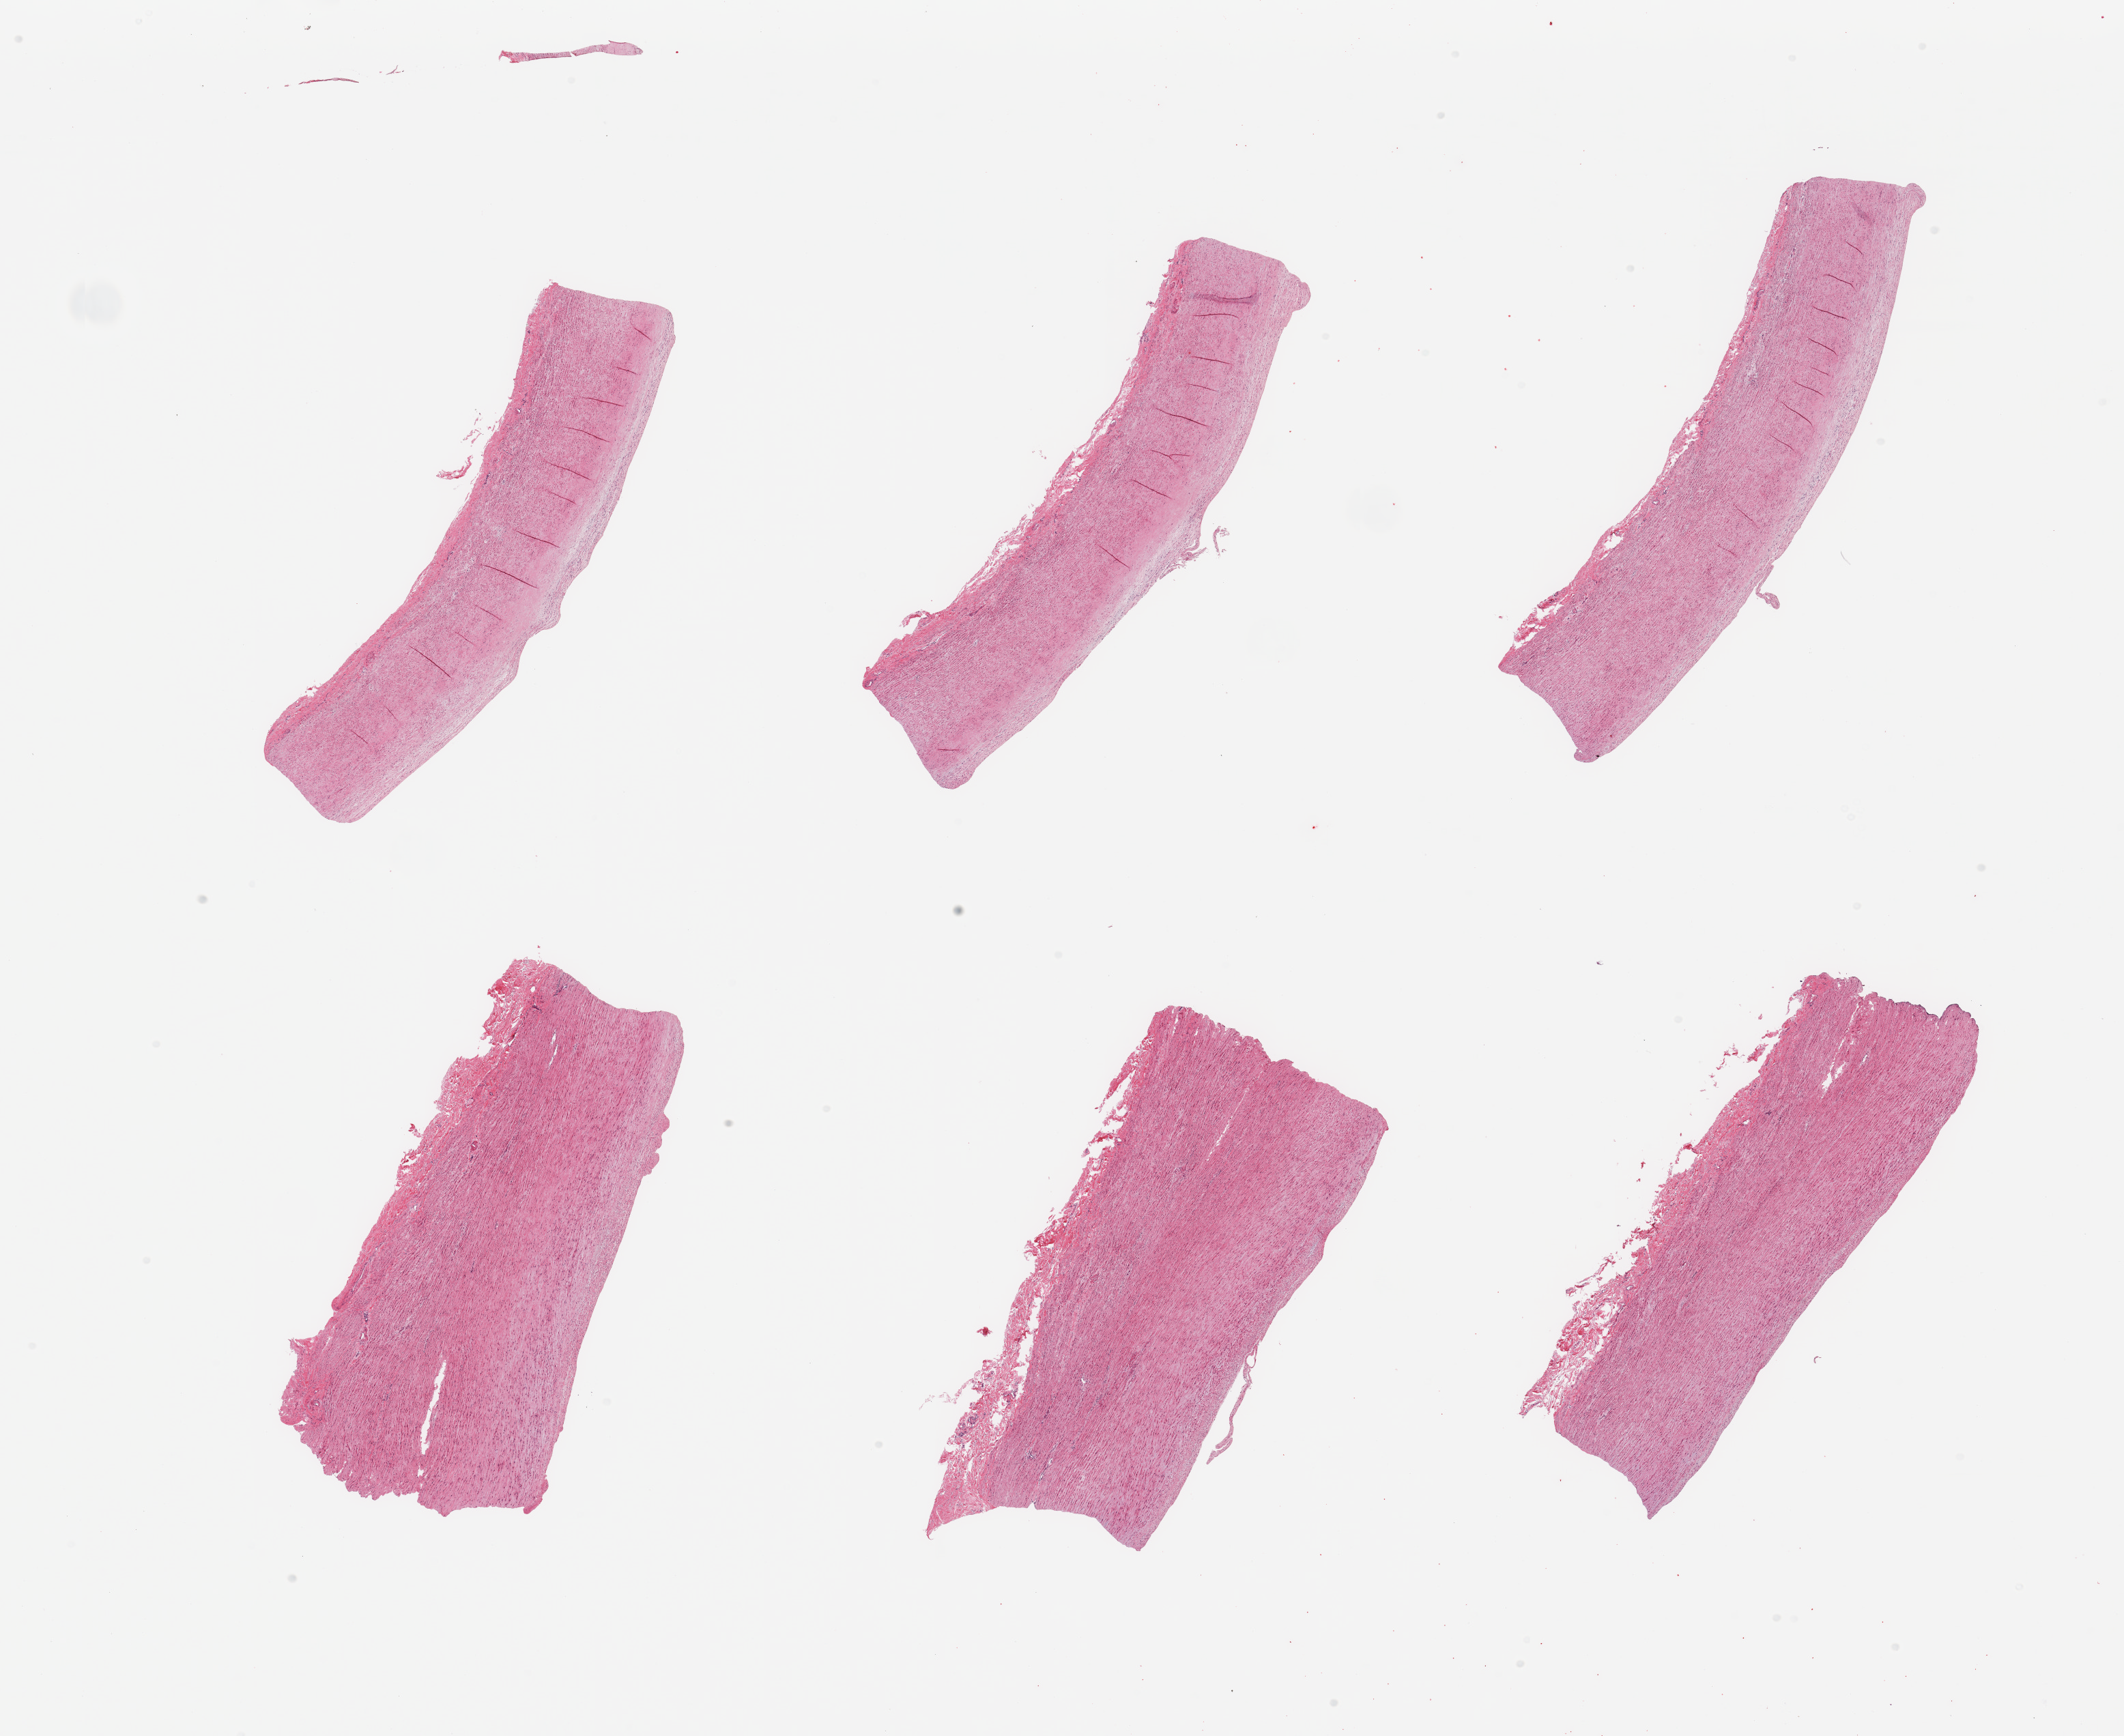
Whole-slide image, H&E stain, brightfield, whole scanned area (about 24.6 x 20.1 mm, acquisition: 20x scan) shown as a low-resolution overview. PAXgene-fixed, paraffin-embedded tissue. Target tissue: aorta. Donor tissue sample. Donor sex: male.
Review note (as recorded): 6 pieces; atherosclerotic plaque.